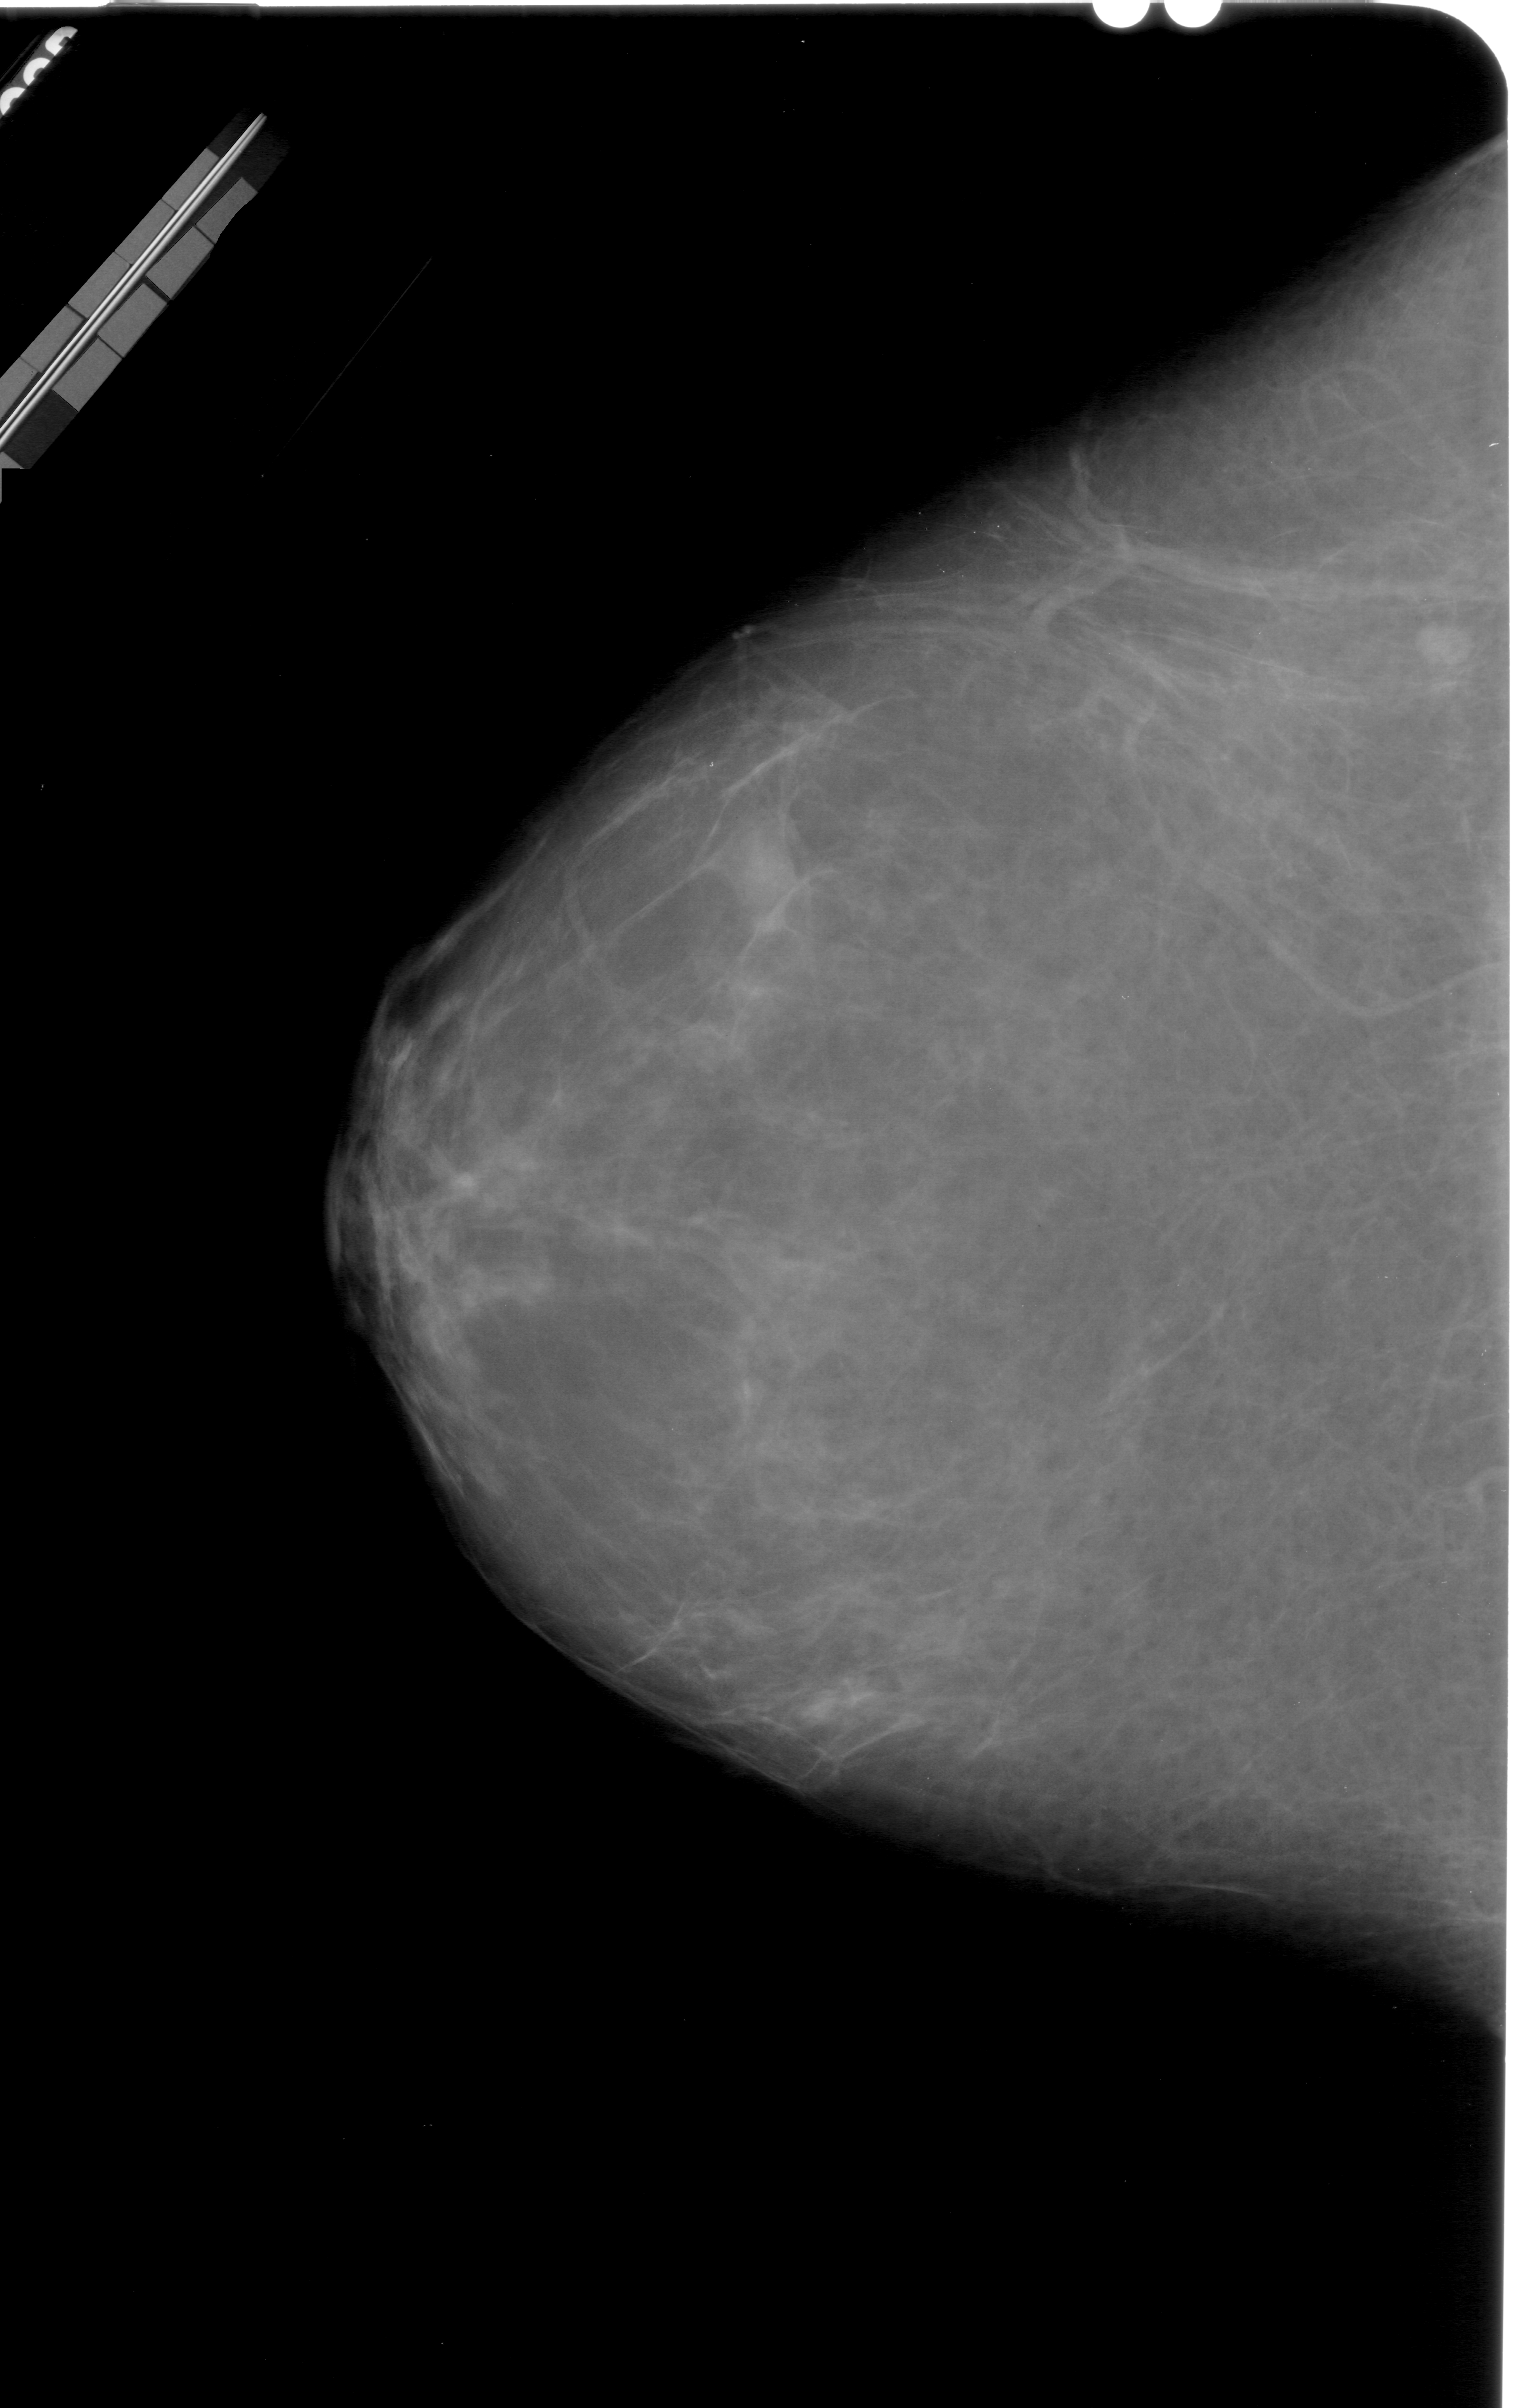
Scanned film-screen mammogram; left breast; craniocaudal (CC) view; 1516 × 2408 image matrix.
Marked abnormalities (boxes around the expert regions of interest):
- mass, shape oval, margins ill defined; BI-RADS assessment category 4; subtlety rating 2 on a 1 (subtle) to 5 (obvious) scale; pathology result (as recorded, not read from the image): benign: bounding box (x1, y1, x2, y2) in pixels: (723, 817, 801, 903)